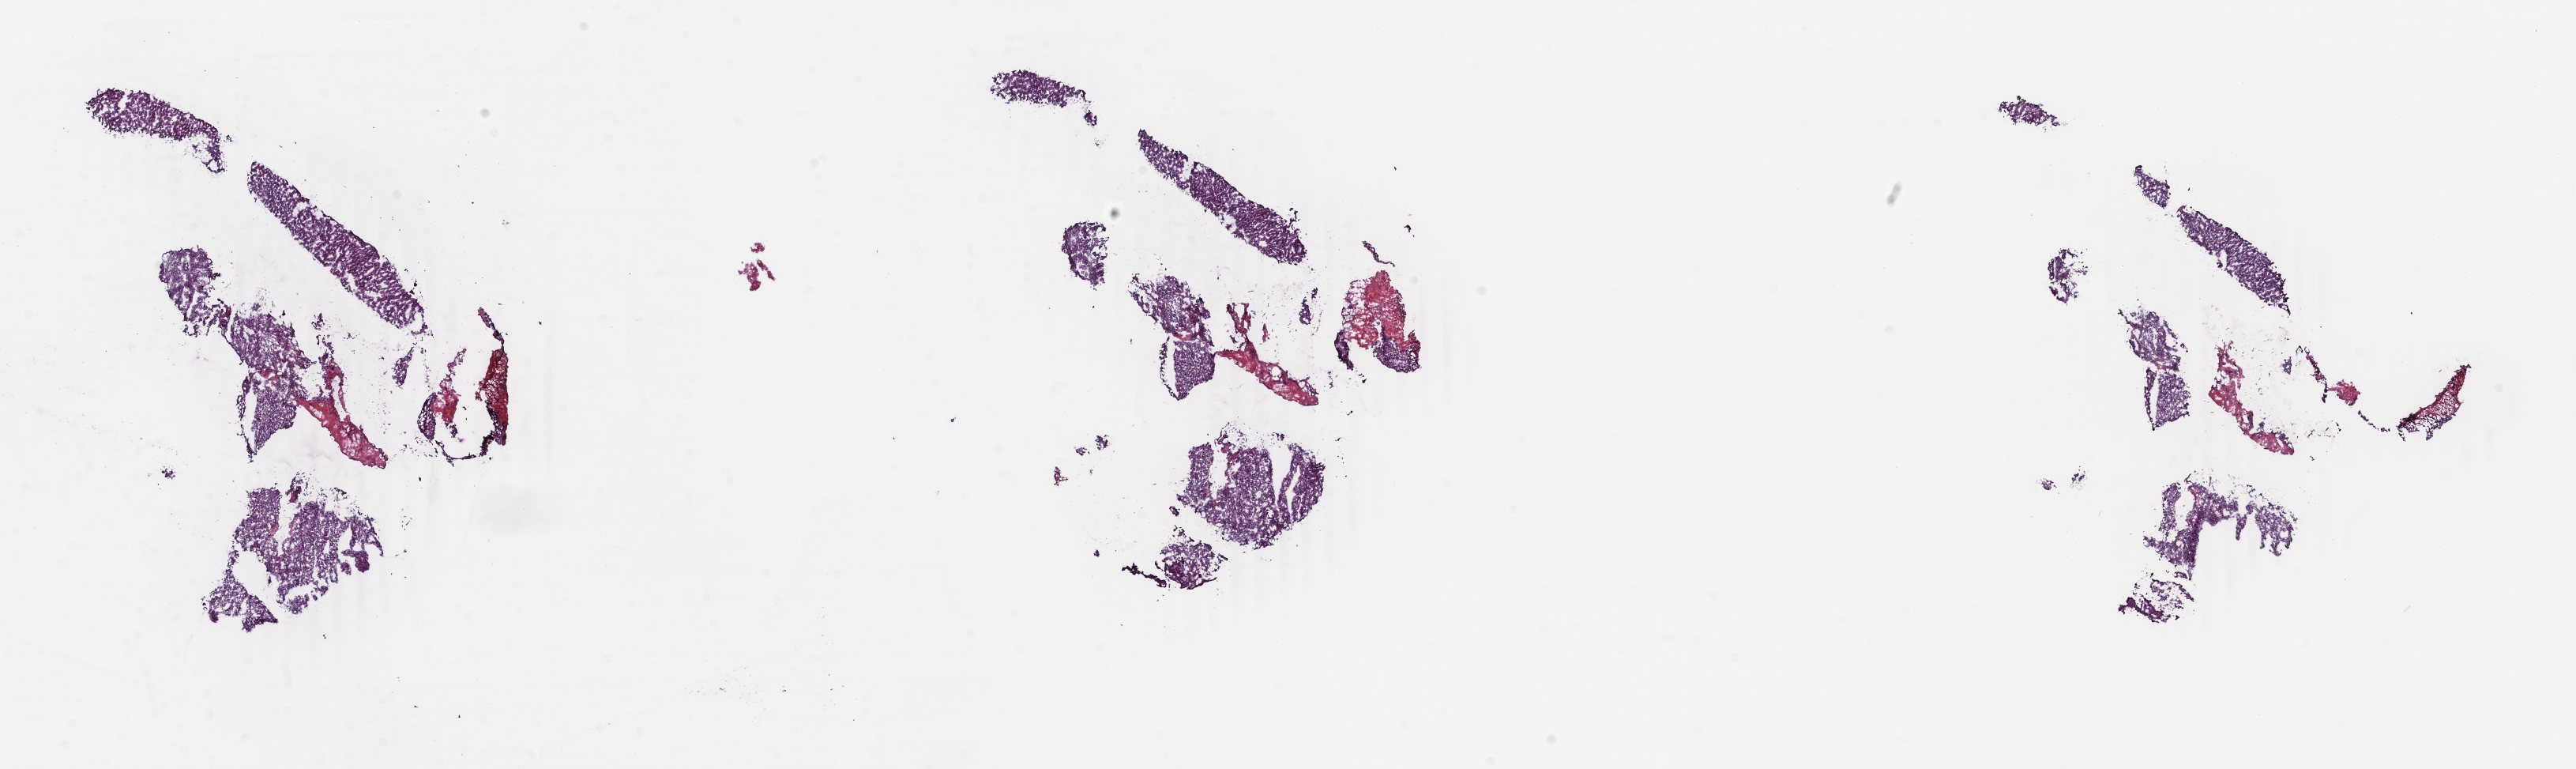
Whole-slide histology image, H&E-stained — shown as a low-resolution overview of the whole scanned area (about 25.9 x 7.7 mm); frozen section from the top of the tissue portion; sample: primary tumour, adrenal cortex. Female, age 27 years at initial diagnosis. Slide review estimates, as recorded: tumour cells 100%, tumour nuclei 80%, normal cells 0%, stromal cells 0%, necrosis 0%. Infiltration values recorded for this section: lymphocyte infiltration 1%, monocyte infiltration 0%, neutrophil infiltration 0%.
Pathologic diagnosis: Adrenal cortical carcinoma (cortex of adrenal gland).